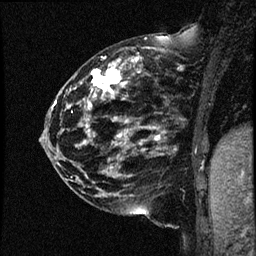
Breast MRI (dynamic contrast-enhanced), one sagittal slice; position 18 of 44 along the scan axis; dynamic contrast-enhanced study with each time point stored as its own series, time point 2 of 4 at this slice position (early post-contrast, ordered by acquisition time); 1.5 T; TE 4.2 ms, TR 17.7 ms; 256 × 256 image matrix, field of view 200 × 200 mm. Female patient, age 52 years. From the clinical record (not read from this slice): setting: breast cancer imaged before/during neoadjuvant chemotherapy; receptor status: HR-positive, HER2-negative.
Outlined on this slice (semi-automatic segmentation, software-assisted and operator-edited):
- analysis volume of interest (the breast-tissue region the enhancement analysis was run in; not a lesion): bounding box [x1, y1, x2, y2] px = [47, 48, 163, 147]
- tumour enhancement mask (voxels above the 100 % enhancement threshold inside the analysis volume of interest): [84, 48, 158, 144]